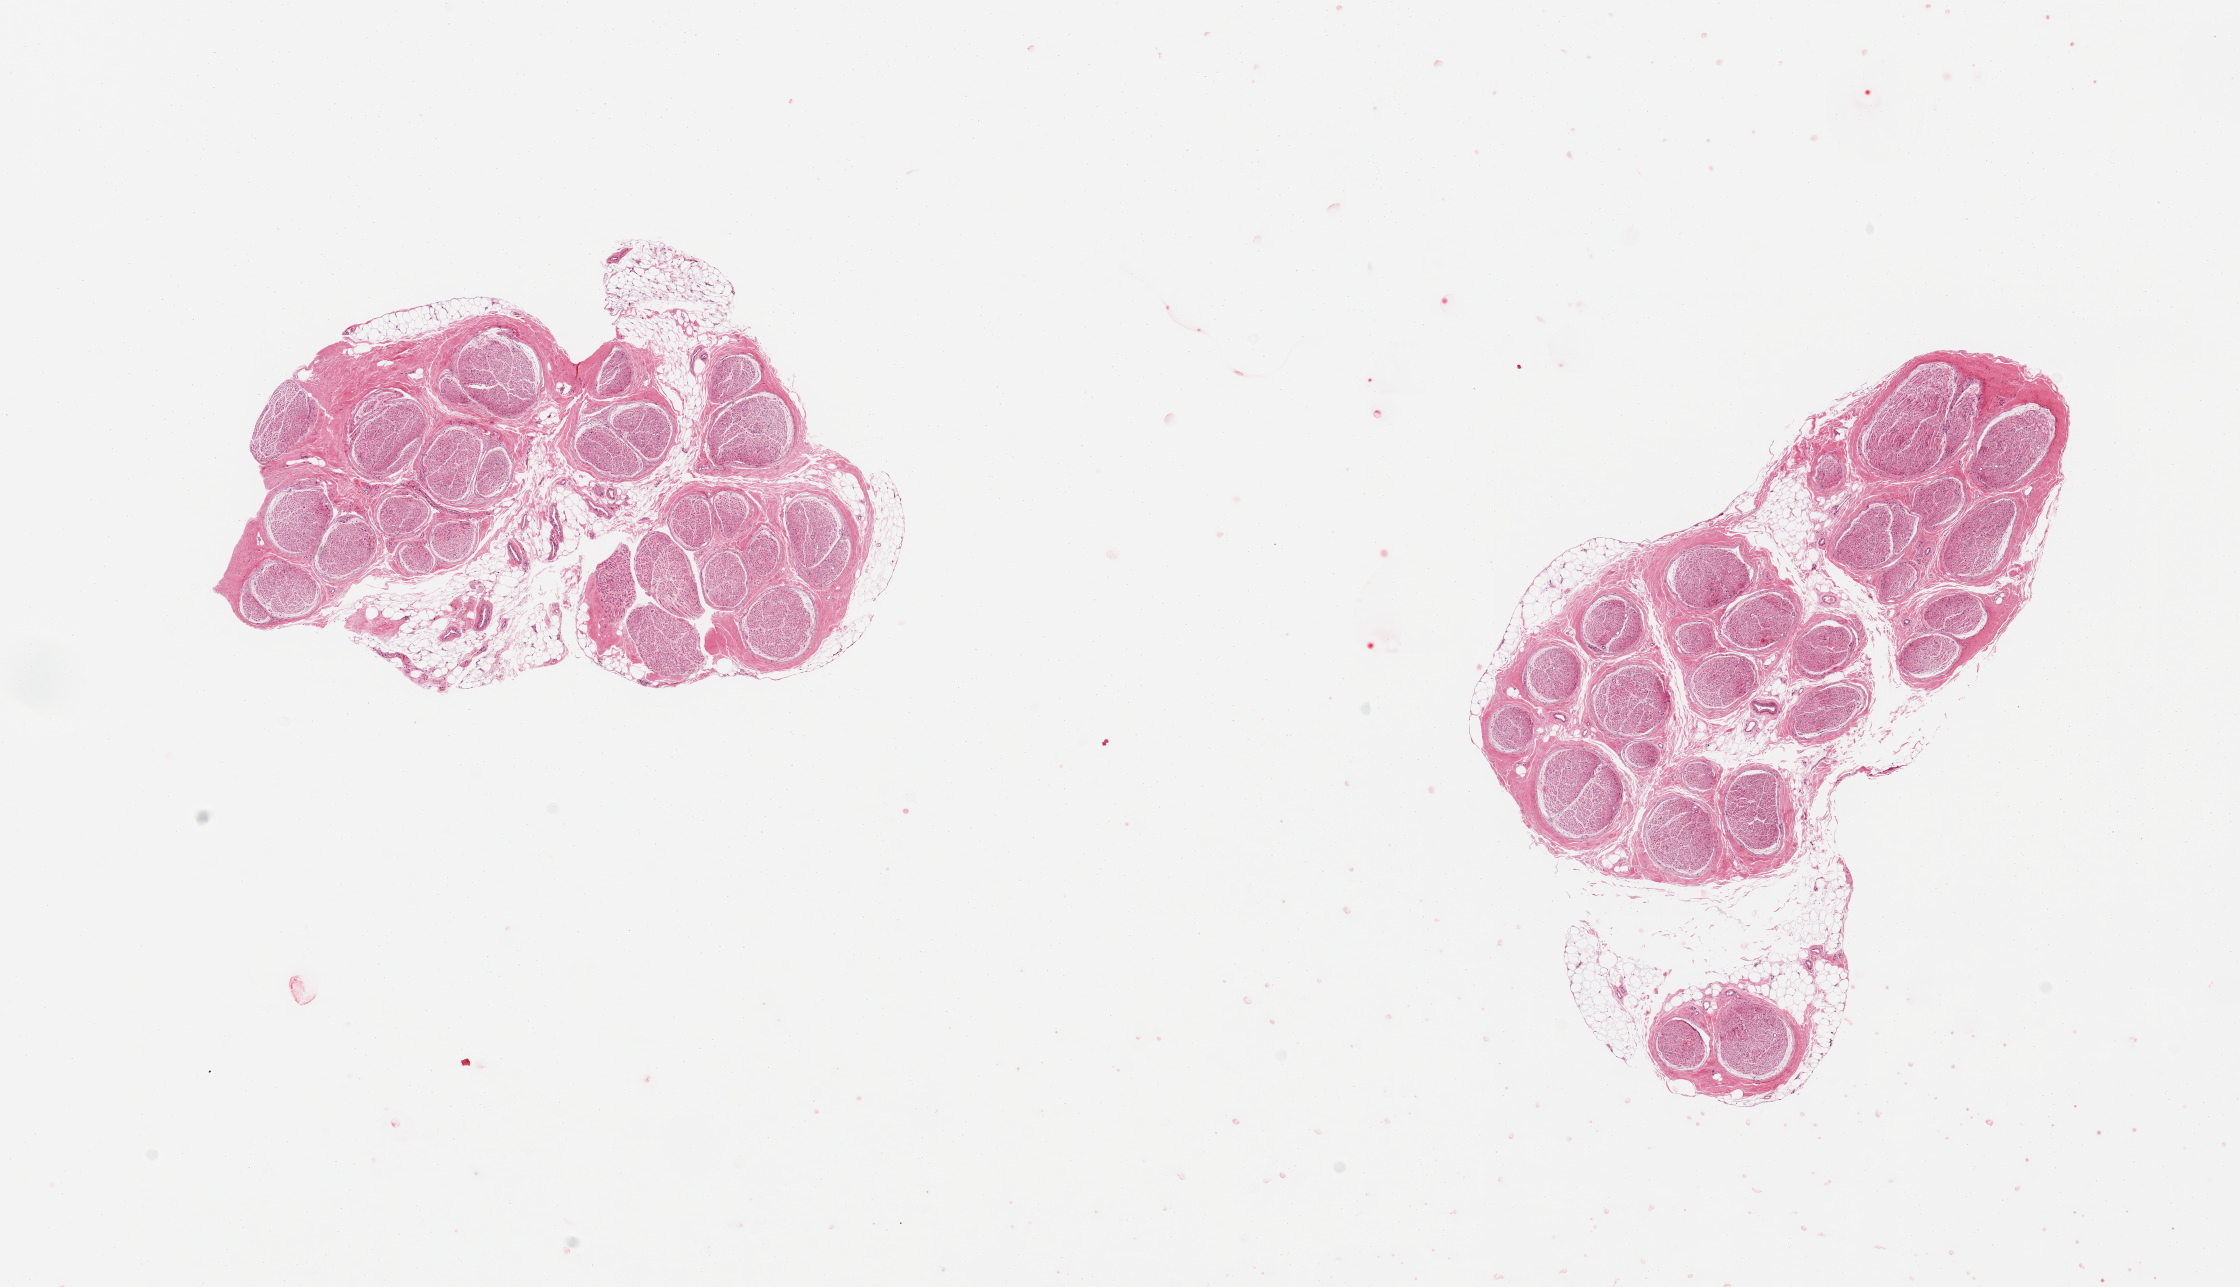
Whole-slide image, haematoxylin and eosin stain, brightfield, whole scanned area (about 17.7 x 10.2 mm) shown as a low-resolution overview. PAXgene-fixed paraffin-embedded (PFPE) section. Target tissue: tibial nerve. Tissue donor sample. Donor sex: female.
Review note (as recorded): 2 pieces; includes 20% internal/external fat.